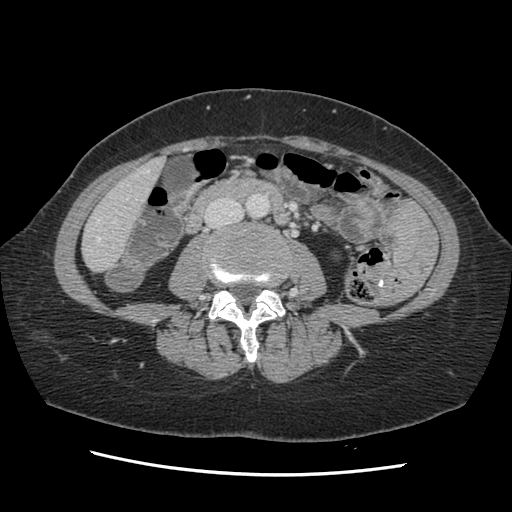
Contrast-enhanced abdominal CT, one axial slice; 120 kVp; soft-tissue window (W 400 / L 40 HU); 2.5 mm slice thickness; 512 × 512 image matrix, field of view 330 × 330 mm. Female patient, age 61 years. Case-level facts recorded for this patient, not image findings: diagnosis: colorectal cancer liver metastases, imaged before liver resection.
Structures marked on this image (manually delineated by an expert):
- hepatic veins: bounding box <97,170,150,241> (left, top, right, bottom; pixels)
- liver: <84,160,162,272>
- planned liver remnant (the part of the liver to remain after resection): <84,161,162,272>